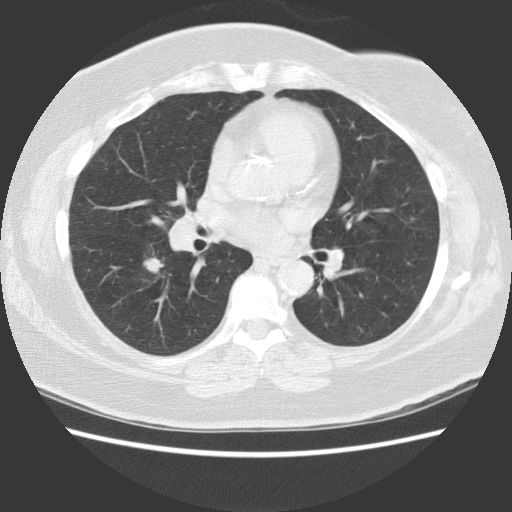
Low-dose screening chest CT, axial slice, baseline annual screen, lung window (W 1500 / L -600 HU), standard (soft-tissue) reconstruction kernel (STANDARD), slice 58 of 117 in the series, 512 × 512 image matrix. Female, age 62 years at enrolment. Former smoker at enrolment.
Expert reader's lesion annotation, bounding box [x1, y1, x2, y2] px = [121, 240, 183, 294]. Reader record for this screening exam (exam-level; its link to the box is not recorded): non-calcified nodule or mass ≥4 mm, right lower lobe, 12 × 10 mm, spiculated (stellate) margins, soft tissue attenuation. Participant outcome: lung cancer diagnosed 182 days after this screen — large cell carcinoma, NOS, right lower lobe, moderately differentiated (G2), stage IA (AJCC 6th edition), 22 mm at pathology.